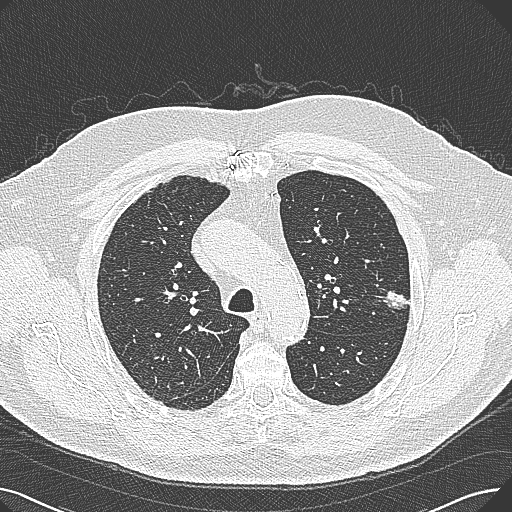
Chest CT (low-dose screening protocol), one axial image. Baseline screening round. Lung window (W 1500 / L -600 HU). Lung (sharp) reconstruction kernel (B80f). Slice 79 of 269 in the series. 512 × 512 image matrix, field of view 370 × 370 mm. Male, age 74 years at enrolment. Former smoker at enrolment.
Expert-annotated lung lesion, bounding box <373,273,423,319> (left, top, right, bottom; pixels). The exam's reader record, not a measurement of the box and not confirmed to be the same lesion: non-calcified nodule or mass ≥4 mm, left upper lobe, 15 × 10 mm, poorly defined margins, soft tissue attenuation. Lung cancer was diagnosed 124 days after this screen: adenocarcinoma, NOS, left upper lobe, well differentiated (G1), stage IA (AJCC 6th edition), 26 mm at pathology.